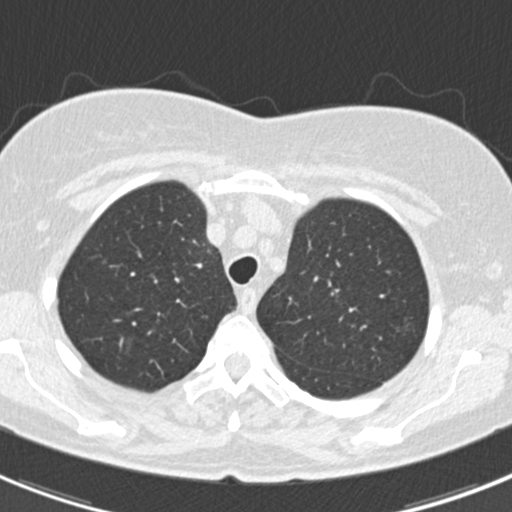
Chest CT (low-dose screening protocol), one axial image; baseline screening round; lung window (W 1500 / L -600 HU); slice 43 of 184 in the series. Female participant, aged 60 years at enrolment. Current smoker at enrolment.
Expert-annotated lung lesion, bounding box (x1, y1, x2, y2) in pixels: (382, 308, 422, 343). The screening reader recorded 3 non-calcified nodules or masses ≥4 mm on this exam; which of them this box marks is not recorded. Official screen result: positive, change unspecified: nodule(s) >= 4 mm or enlarging nodule(s), mass(es), or other non-specific abnormalities suspicious for lung cancer.